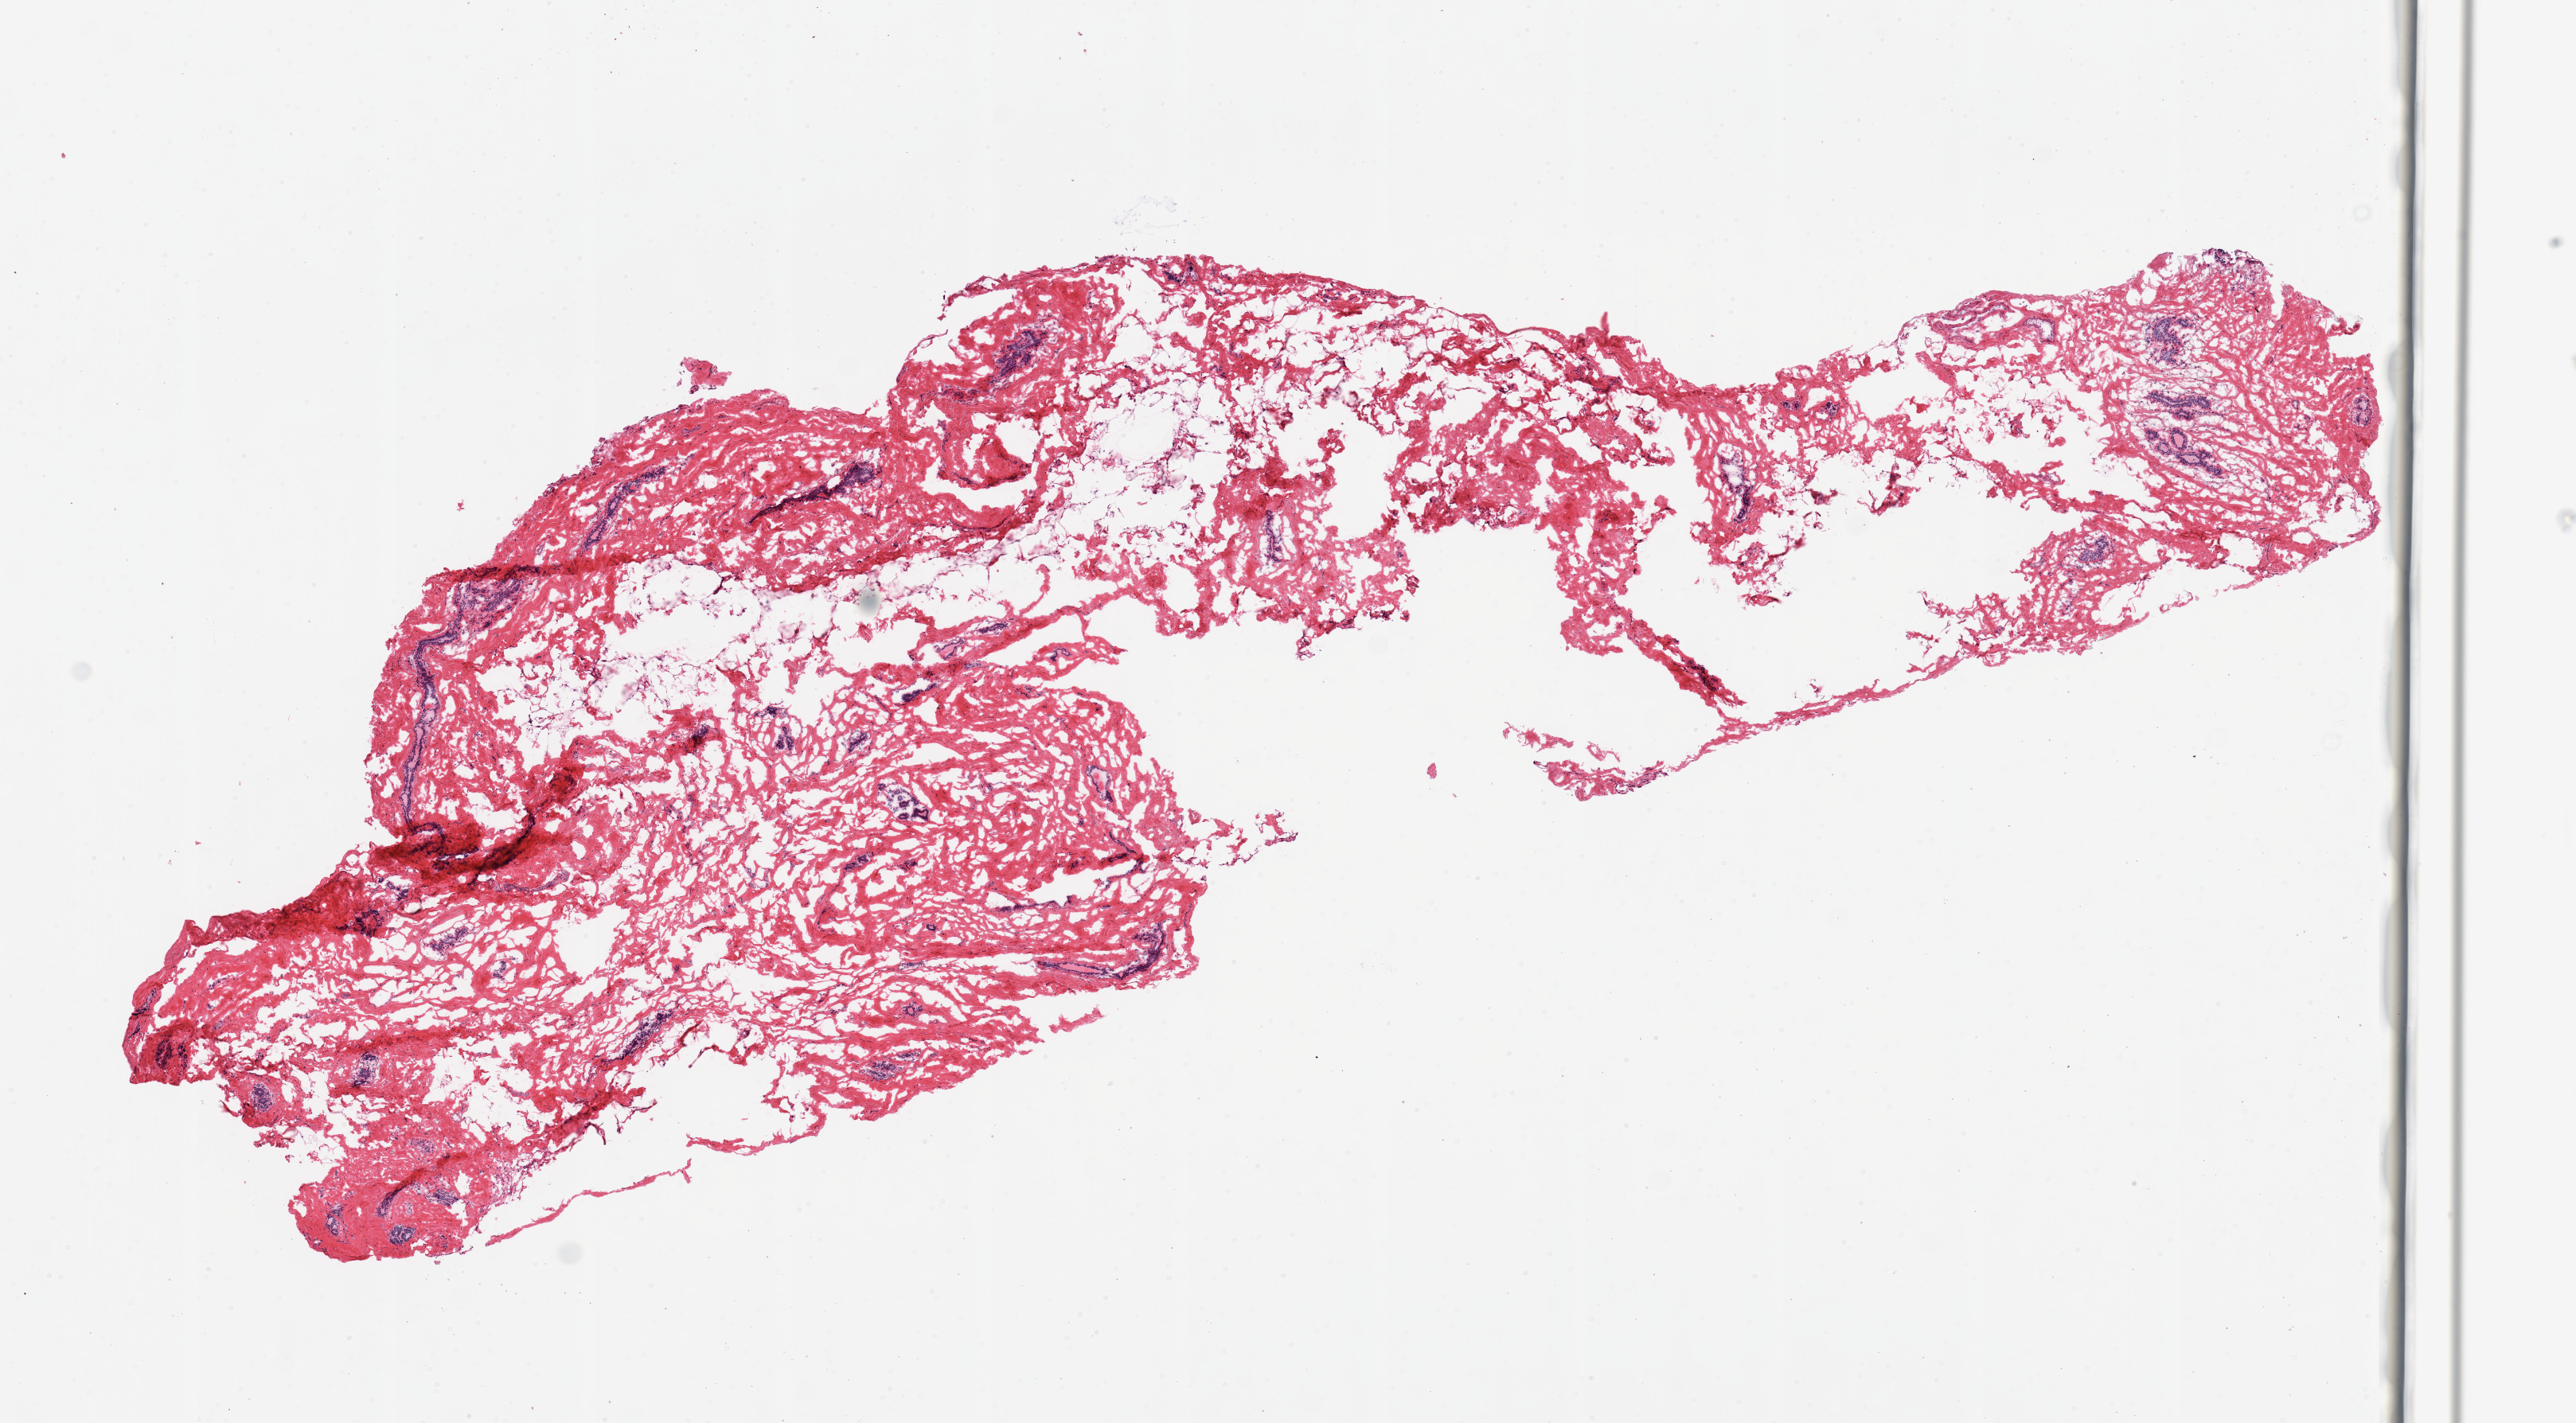
Digitized H&E-stained section, brightfield, low-resolution overview of the scanned area, about 12.8 x 7.1 mm. Frozen section (dry ice). Section of breast (target tissue). Tissue donor sample. Donor sex: female.
• review note (as recorded): 1 piece